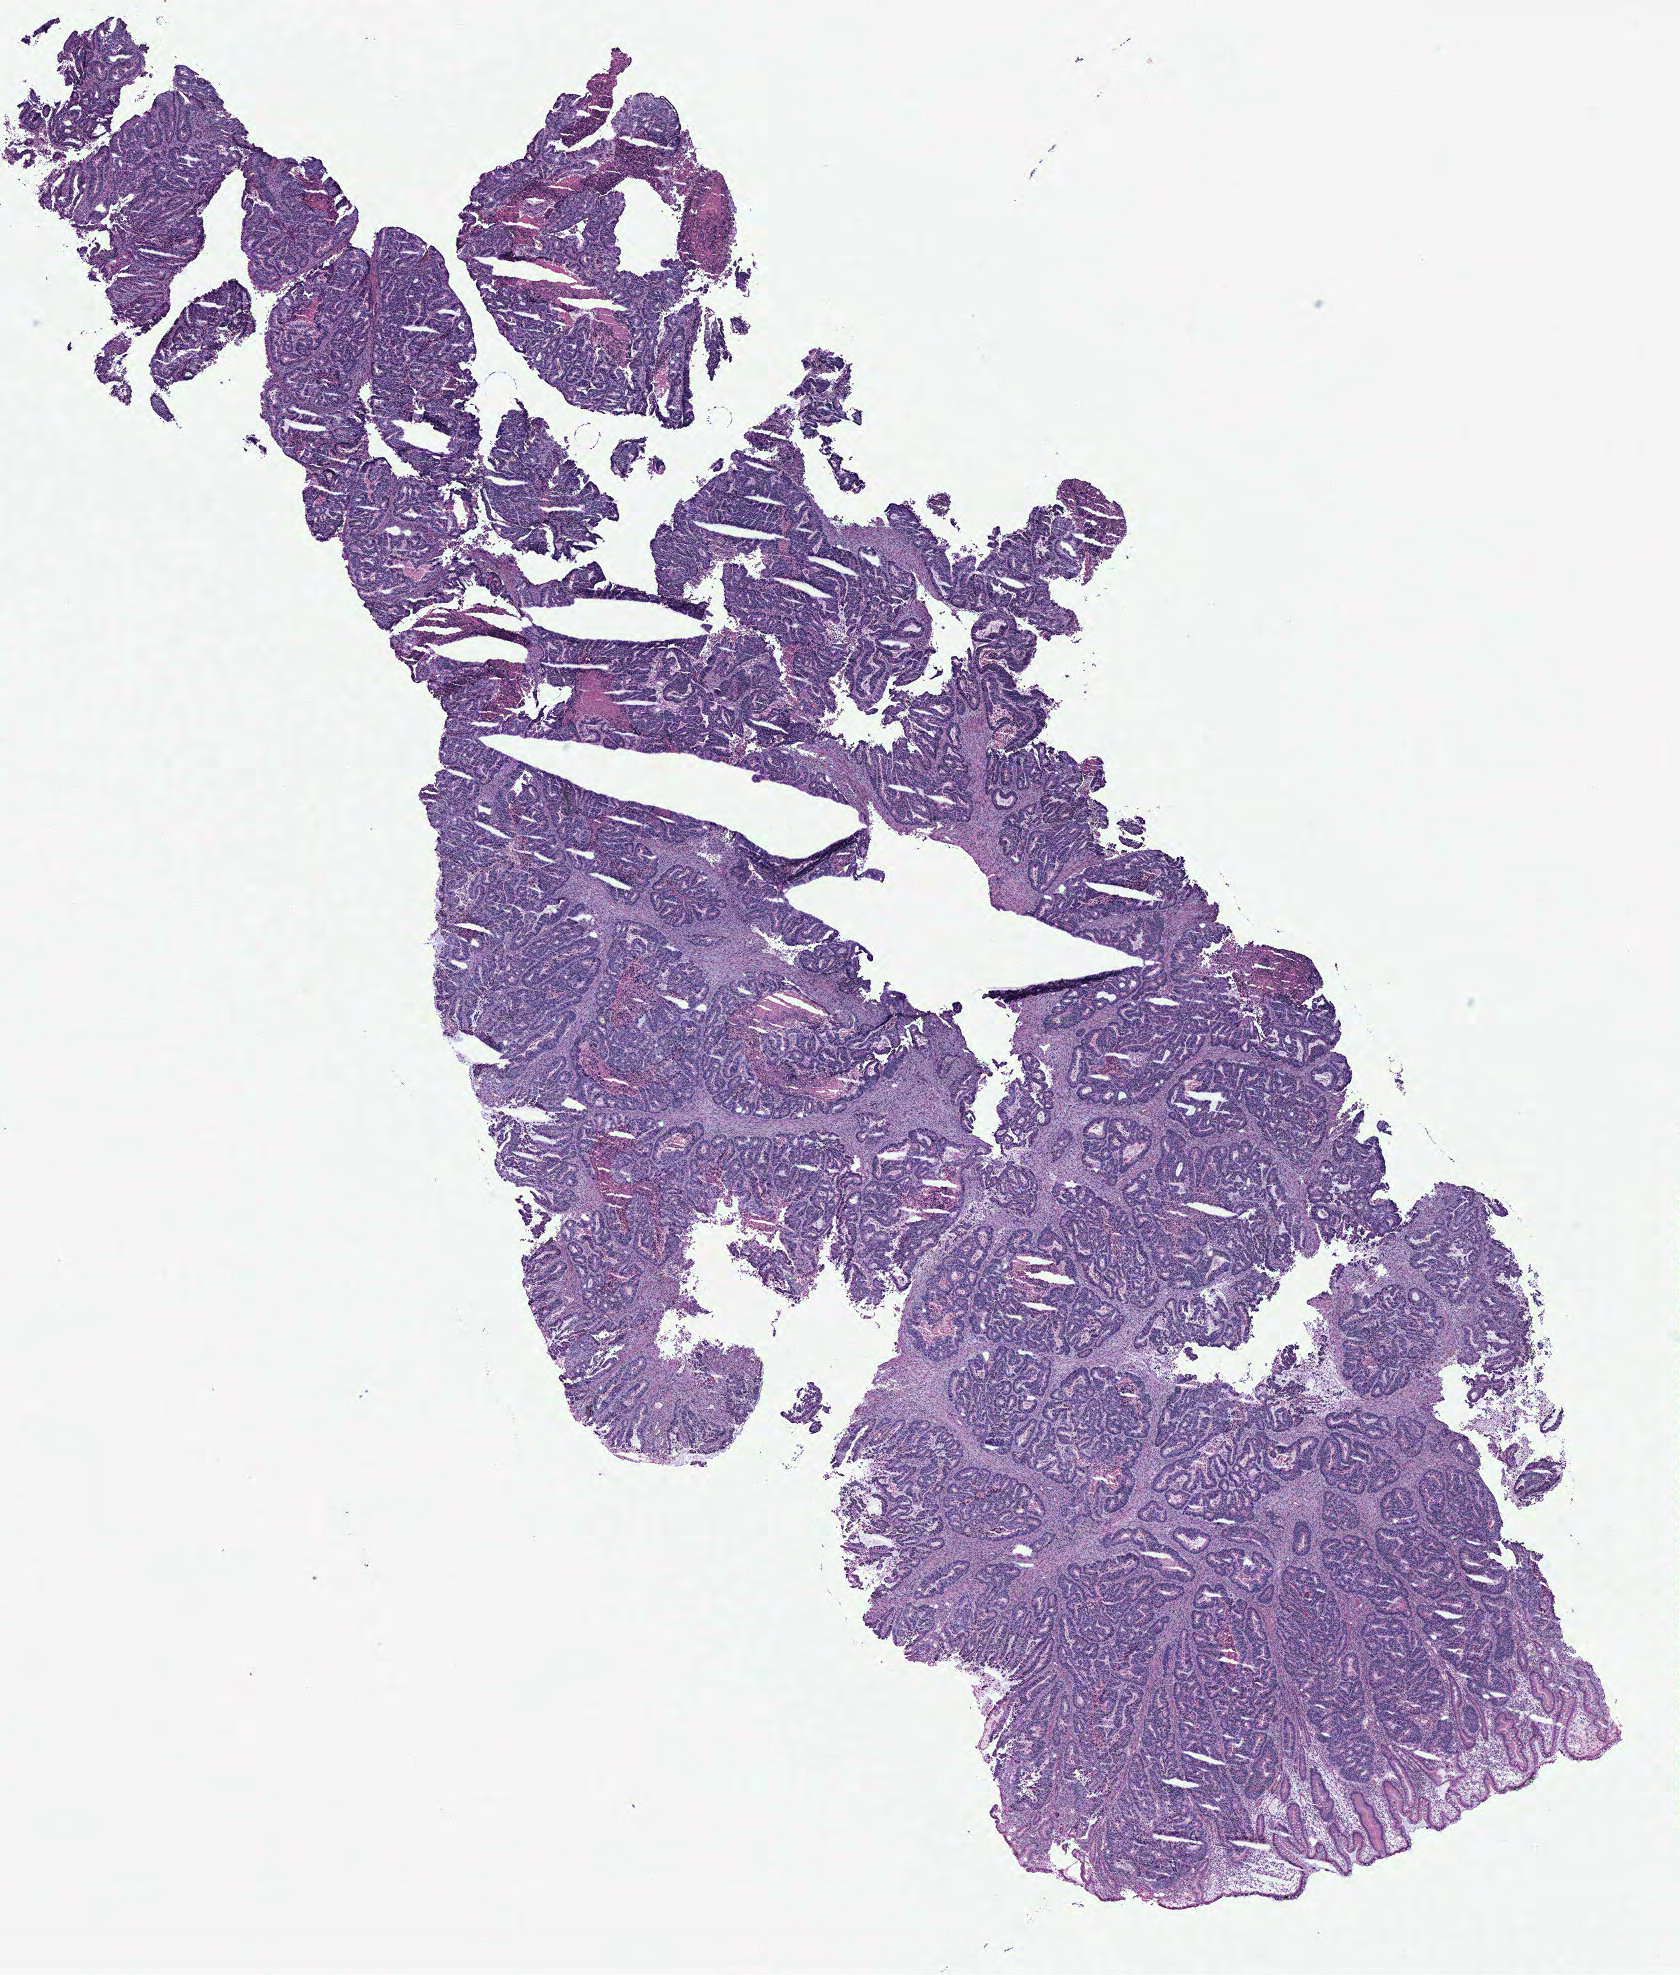
Hematoxylin and eosin (H&E) stained whole-slide image, whole scanned area (about 13.4 x 15.8 mm) shown as a low-resolution overview; normal (non-tumour) tissue sample, colon. 88-year-old male patient.
This section: normal (non-tumour) tissue from the same patient. Patient diagnosis: Adenocarcinoma, NOS.